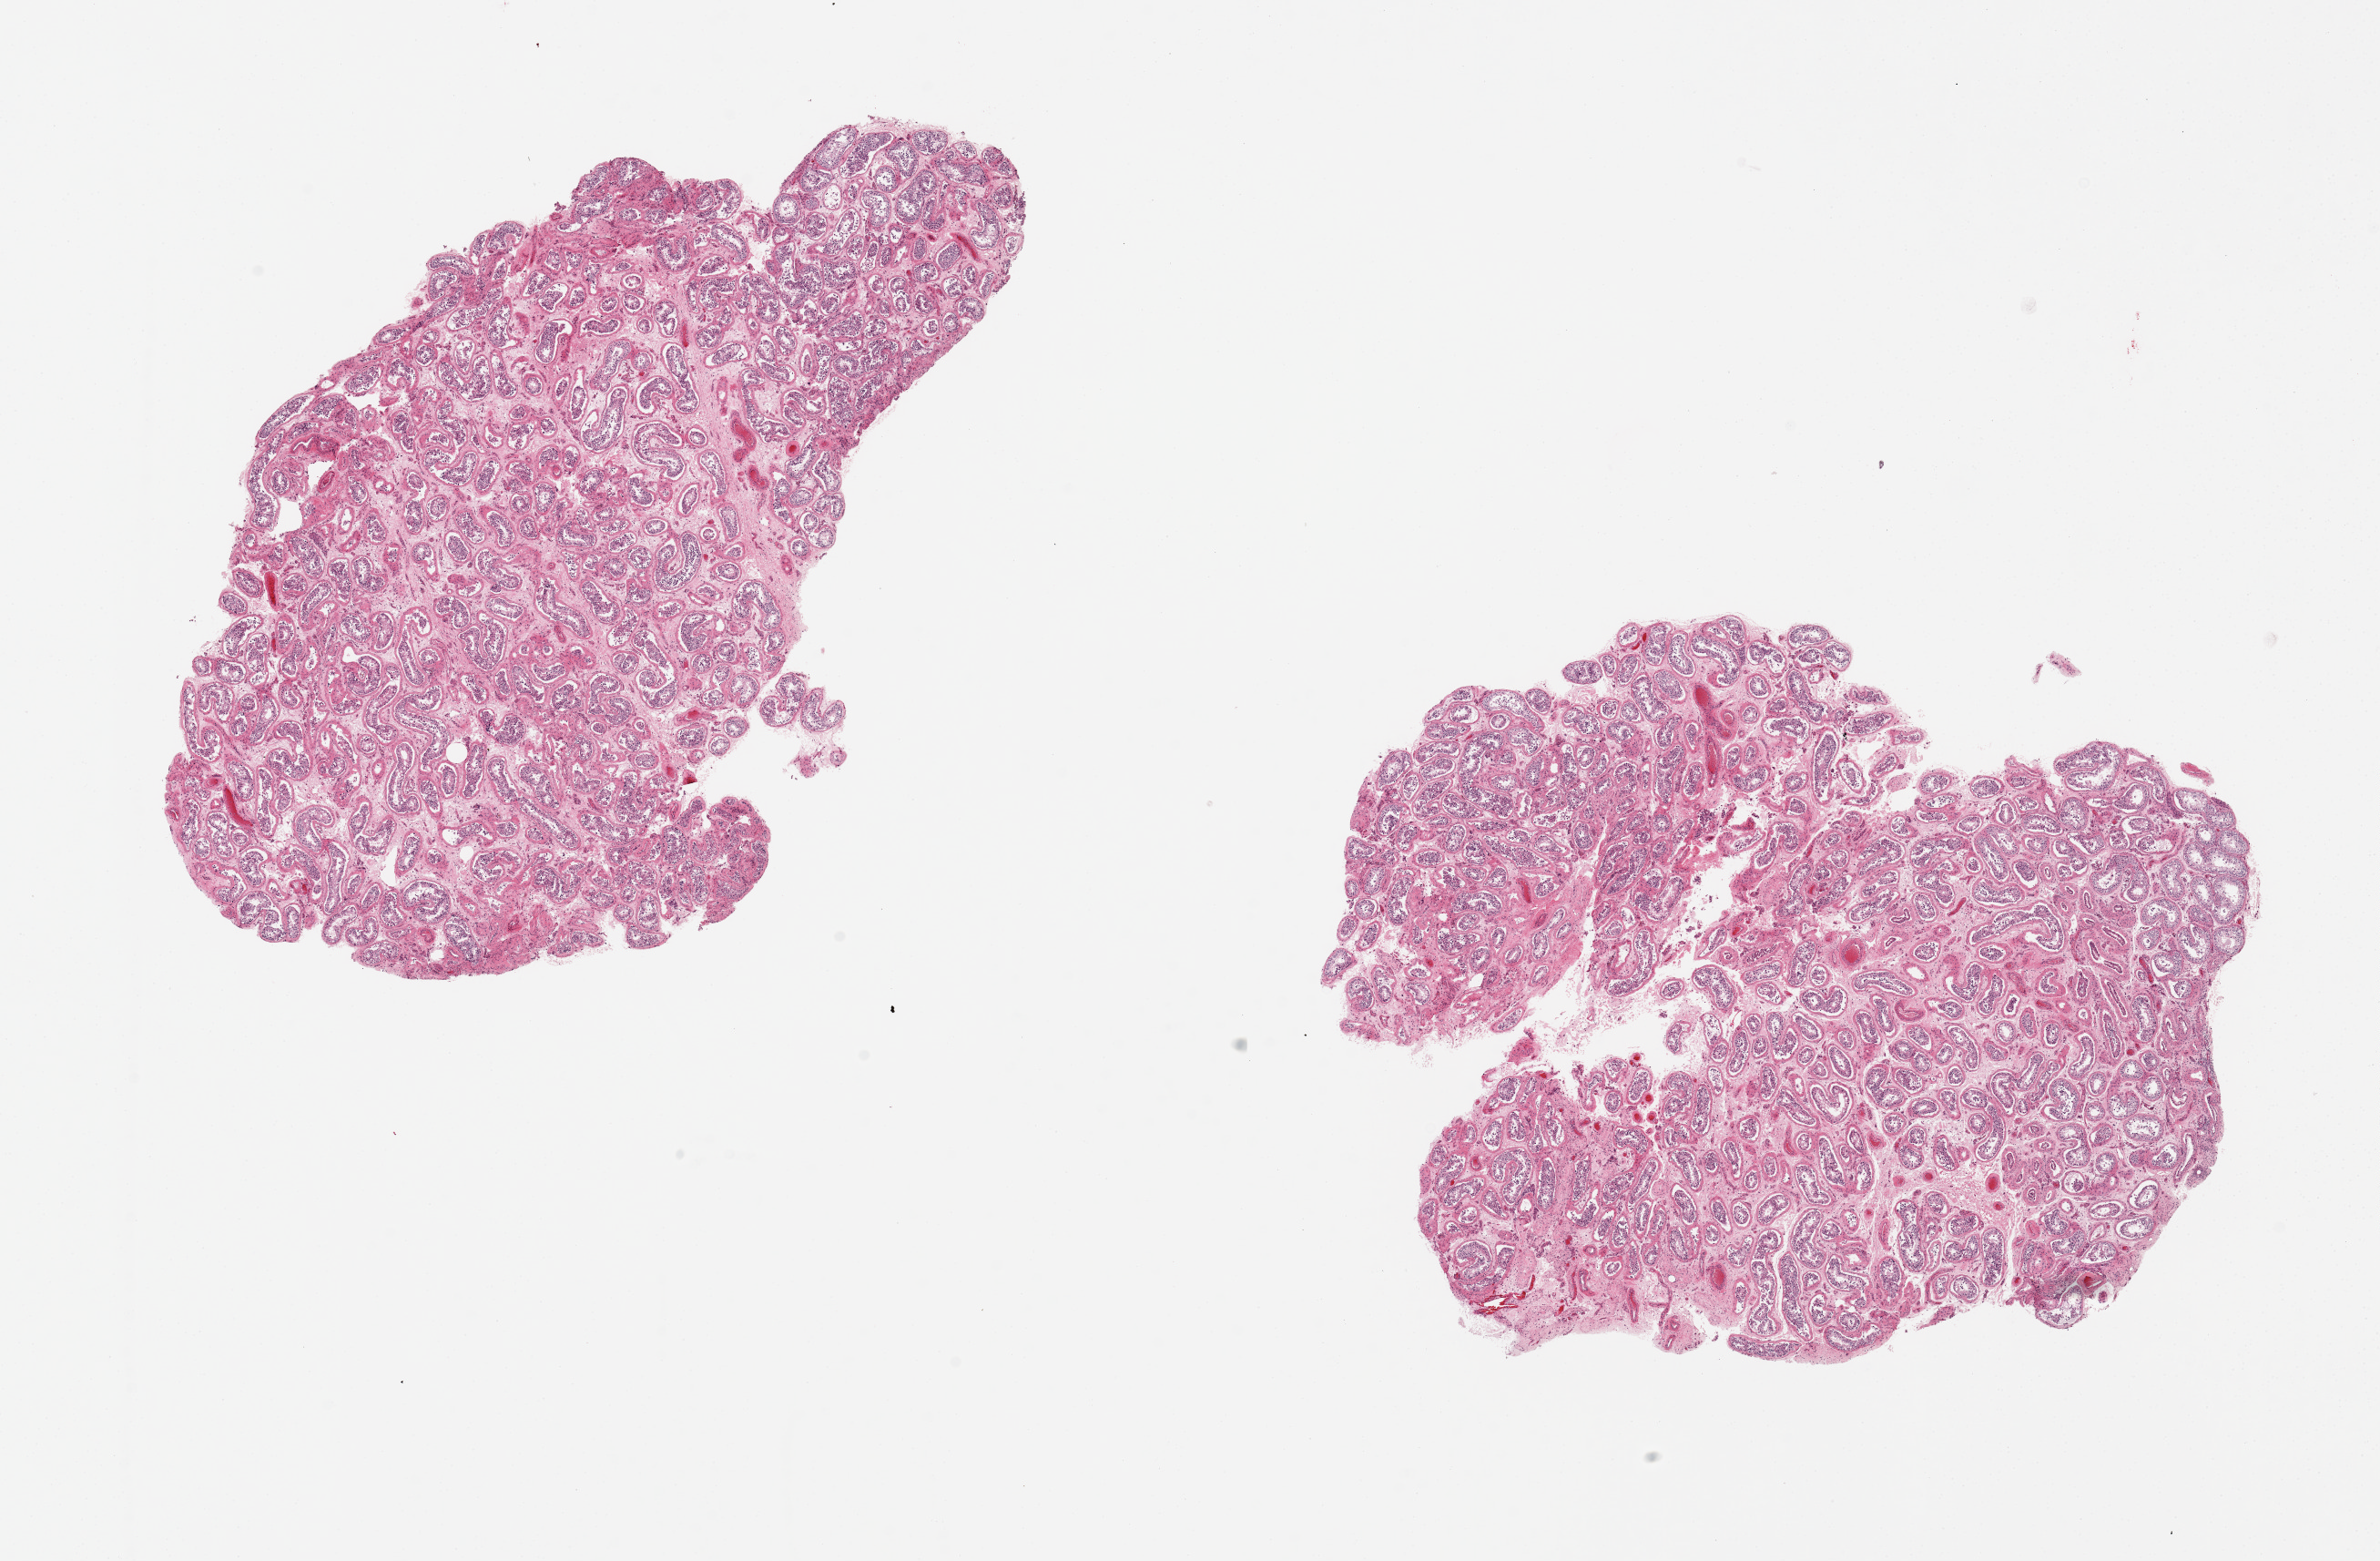
Hematoxylin and eosin (H&E) whole-slide image, brightfield — shown as a low-resolution overview of the whole scanned area (about 20.7 x 13.6 mm, acquisition: 20x scan). PAXgene-fixed, paraffin-embedded tissue. Sampled site (target tissue): testis. Donor tissue sample. Donor: male.
Pathologist's review note for this sample: 2 pieces, 9x6 and 8x7mm; spermatogenesis is present but tubules moderately-markedly autolyzed.